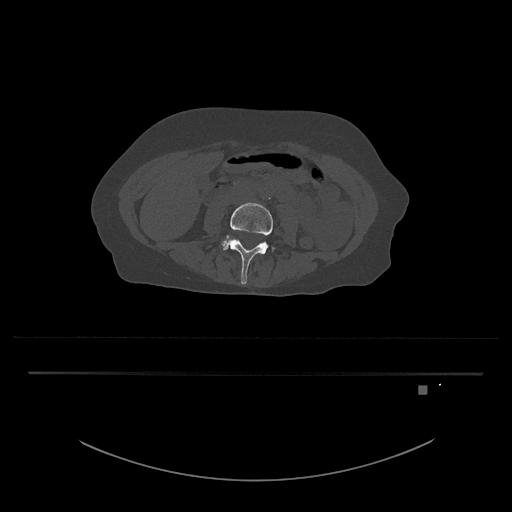
CT including the spine, one axial slice. Position 360 of 797 along the scan axis. 120 kVp. Bone window (W 1800 / L 400 HU). 0.5 mm slice thickness. 512 × 512 image matrix, field of view 500 × 500 mm. Patient: female, 57 years. From the clinical record (not read from this slice): primary cancer: cervical.
Outlined on this slice (semi-automatic segmentation, software-assisted and operator-edited):
- L4 vertebra: bounding box (x1, y1, x2, y2) in pixels: (223, 202, 275, 284)